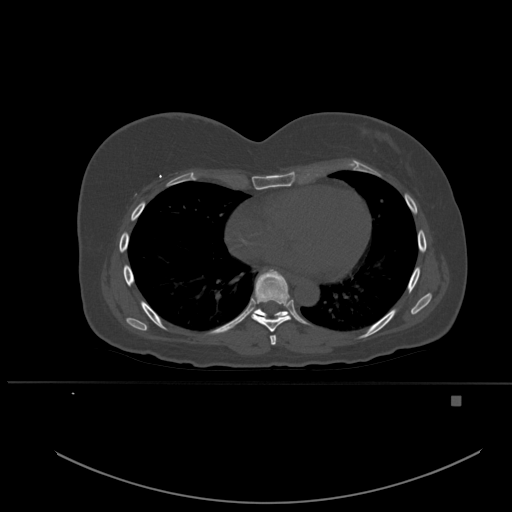
CT including the spine, one axial slice; position 331 of 651 along the scan axis; bone window (W 1800 / L 400 HU); 512 × 512 image matrix. Female patient, age 49 years. From the clinical record (not read from this slice): primary cancer: breast; vertebrae with lytic lesions (as recorded): L3, T12, L4.
Outlined on this slice (semi-automatic segmentation, software-assisted and operator-edited):
- T6 vertebra: box from (x=270, y=335) to (x=277, y=345) px
- T7 vertebra: (x=251, y=269)–(x=294, y=332)
- T8 vertebra: (x=253, y=270)–(x=288, y=318)